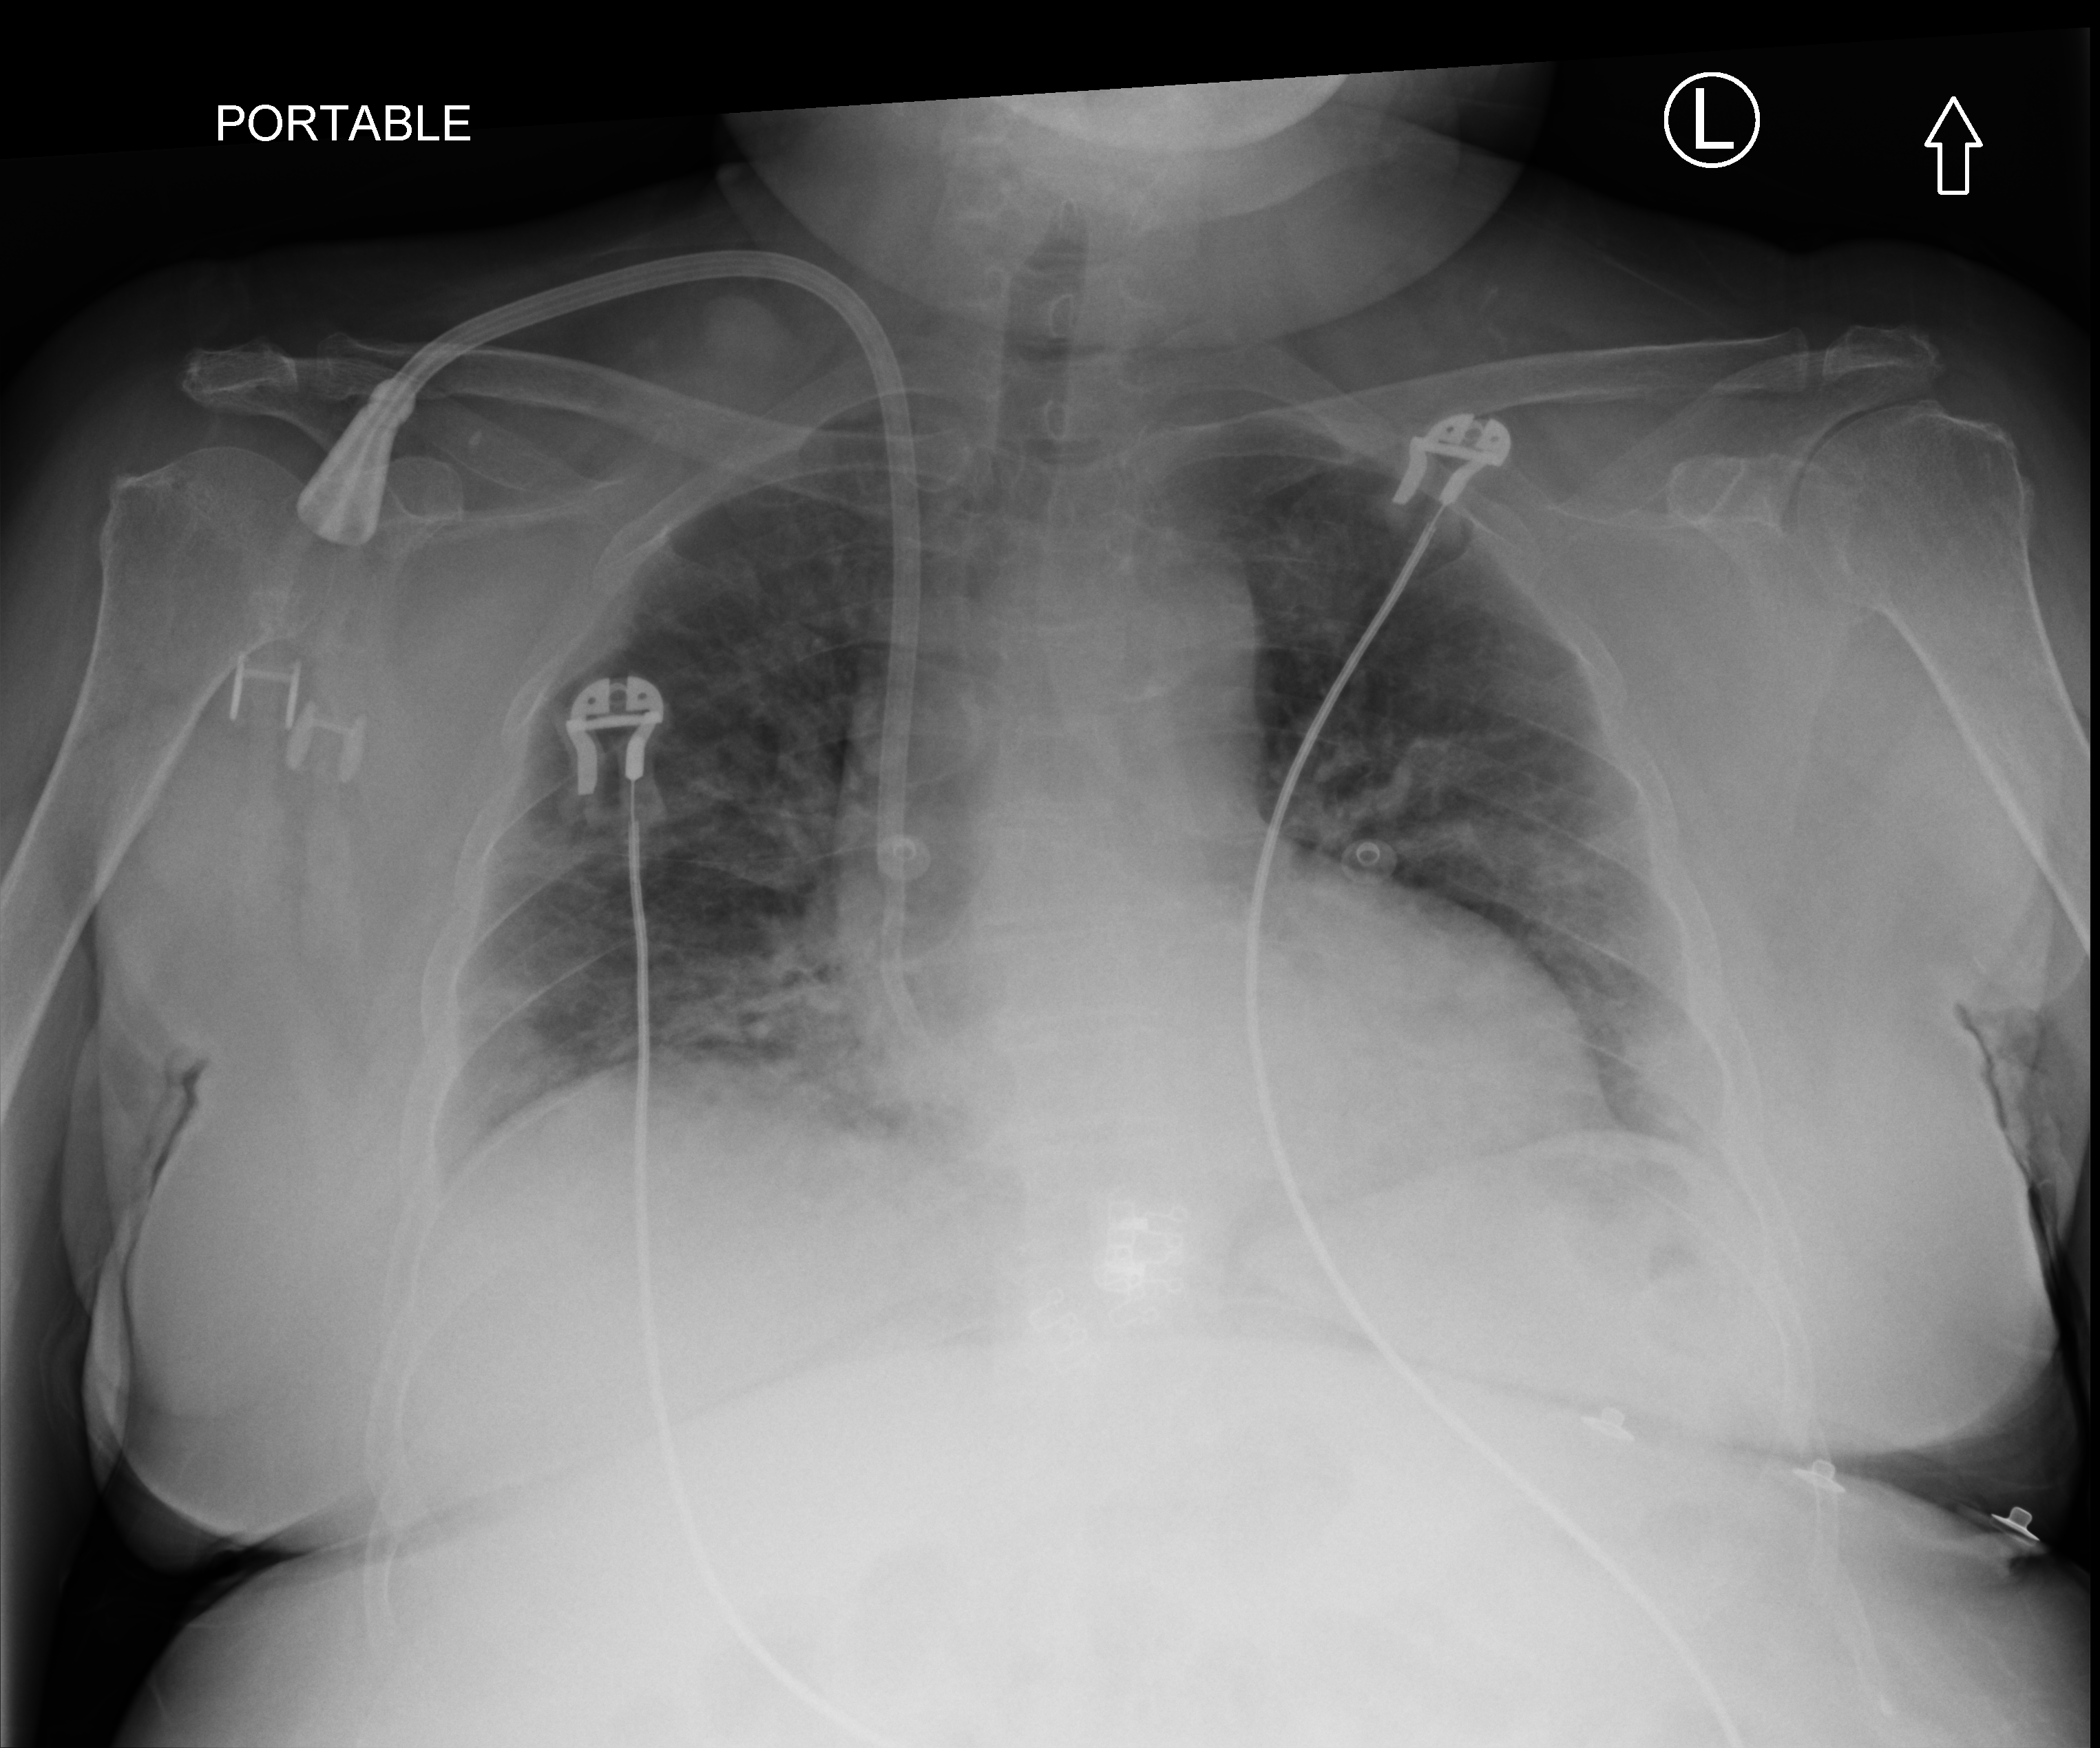
Portable chest radiograph, anteroposterior (AP) projection. Patient hospitalised with COVID-19; female, aged 60–74 years.
Admission-level facts for this patient (not findings on this image; timing relative to this image not recorded):
- hypertension (admission record): yes